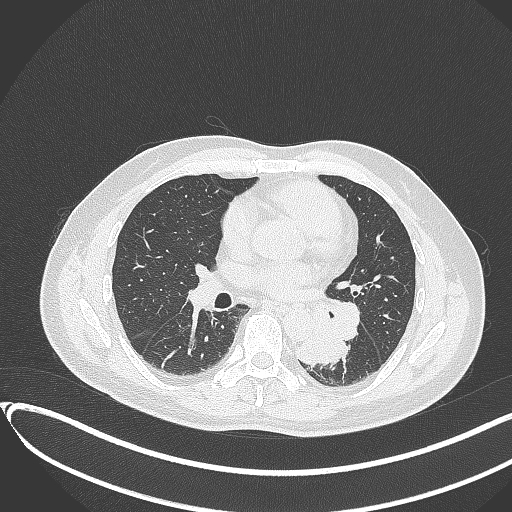
Chest CT, one axial slice. Position 173 of 417 along the scan axis. Lung window (W 1500 / L -600 HU). 512 × 512 image matrix, field of view 400 × 400 mm. Patient: male, 54 years. From the clinical record (not read from this slice): clinical TNM (as recorded): T3 N0 M0.
Structures marked on this image (rectangle marked by the reading radiologist):
- lung tumour (recorded histology: squamous cell carcinoma): bounding box [x1, y1, x2, y2] px = [290, 319, 352, 366]